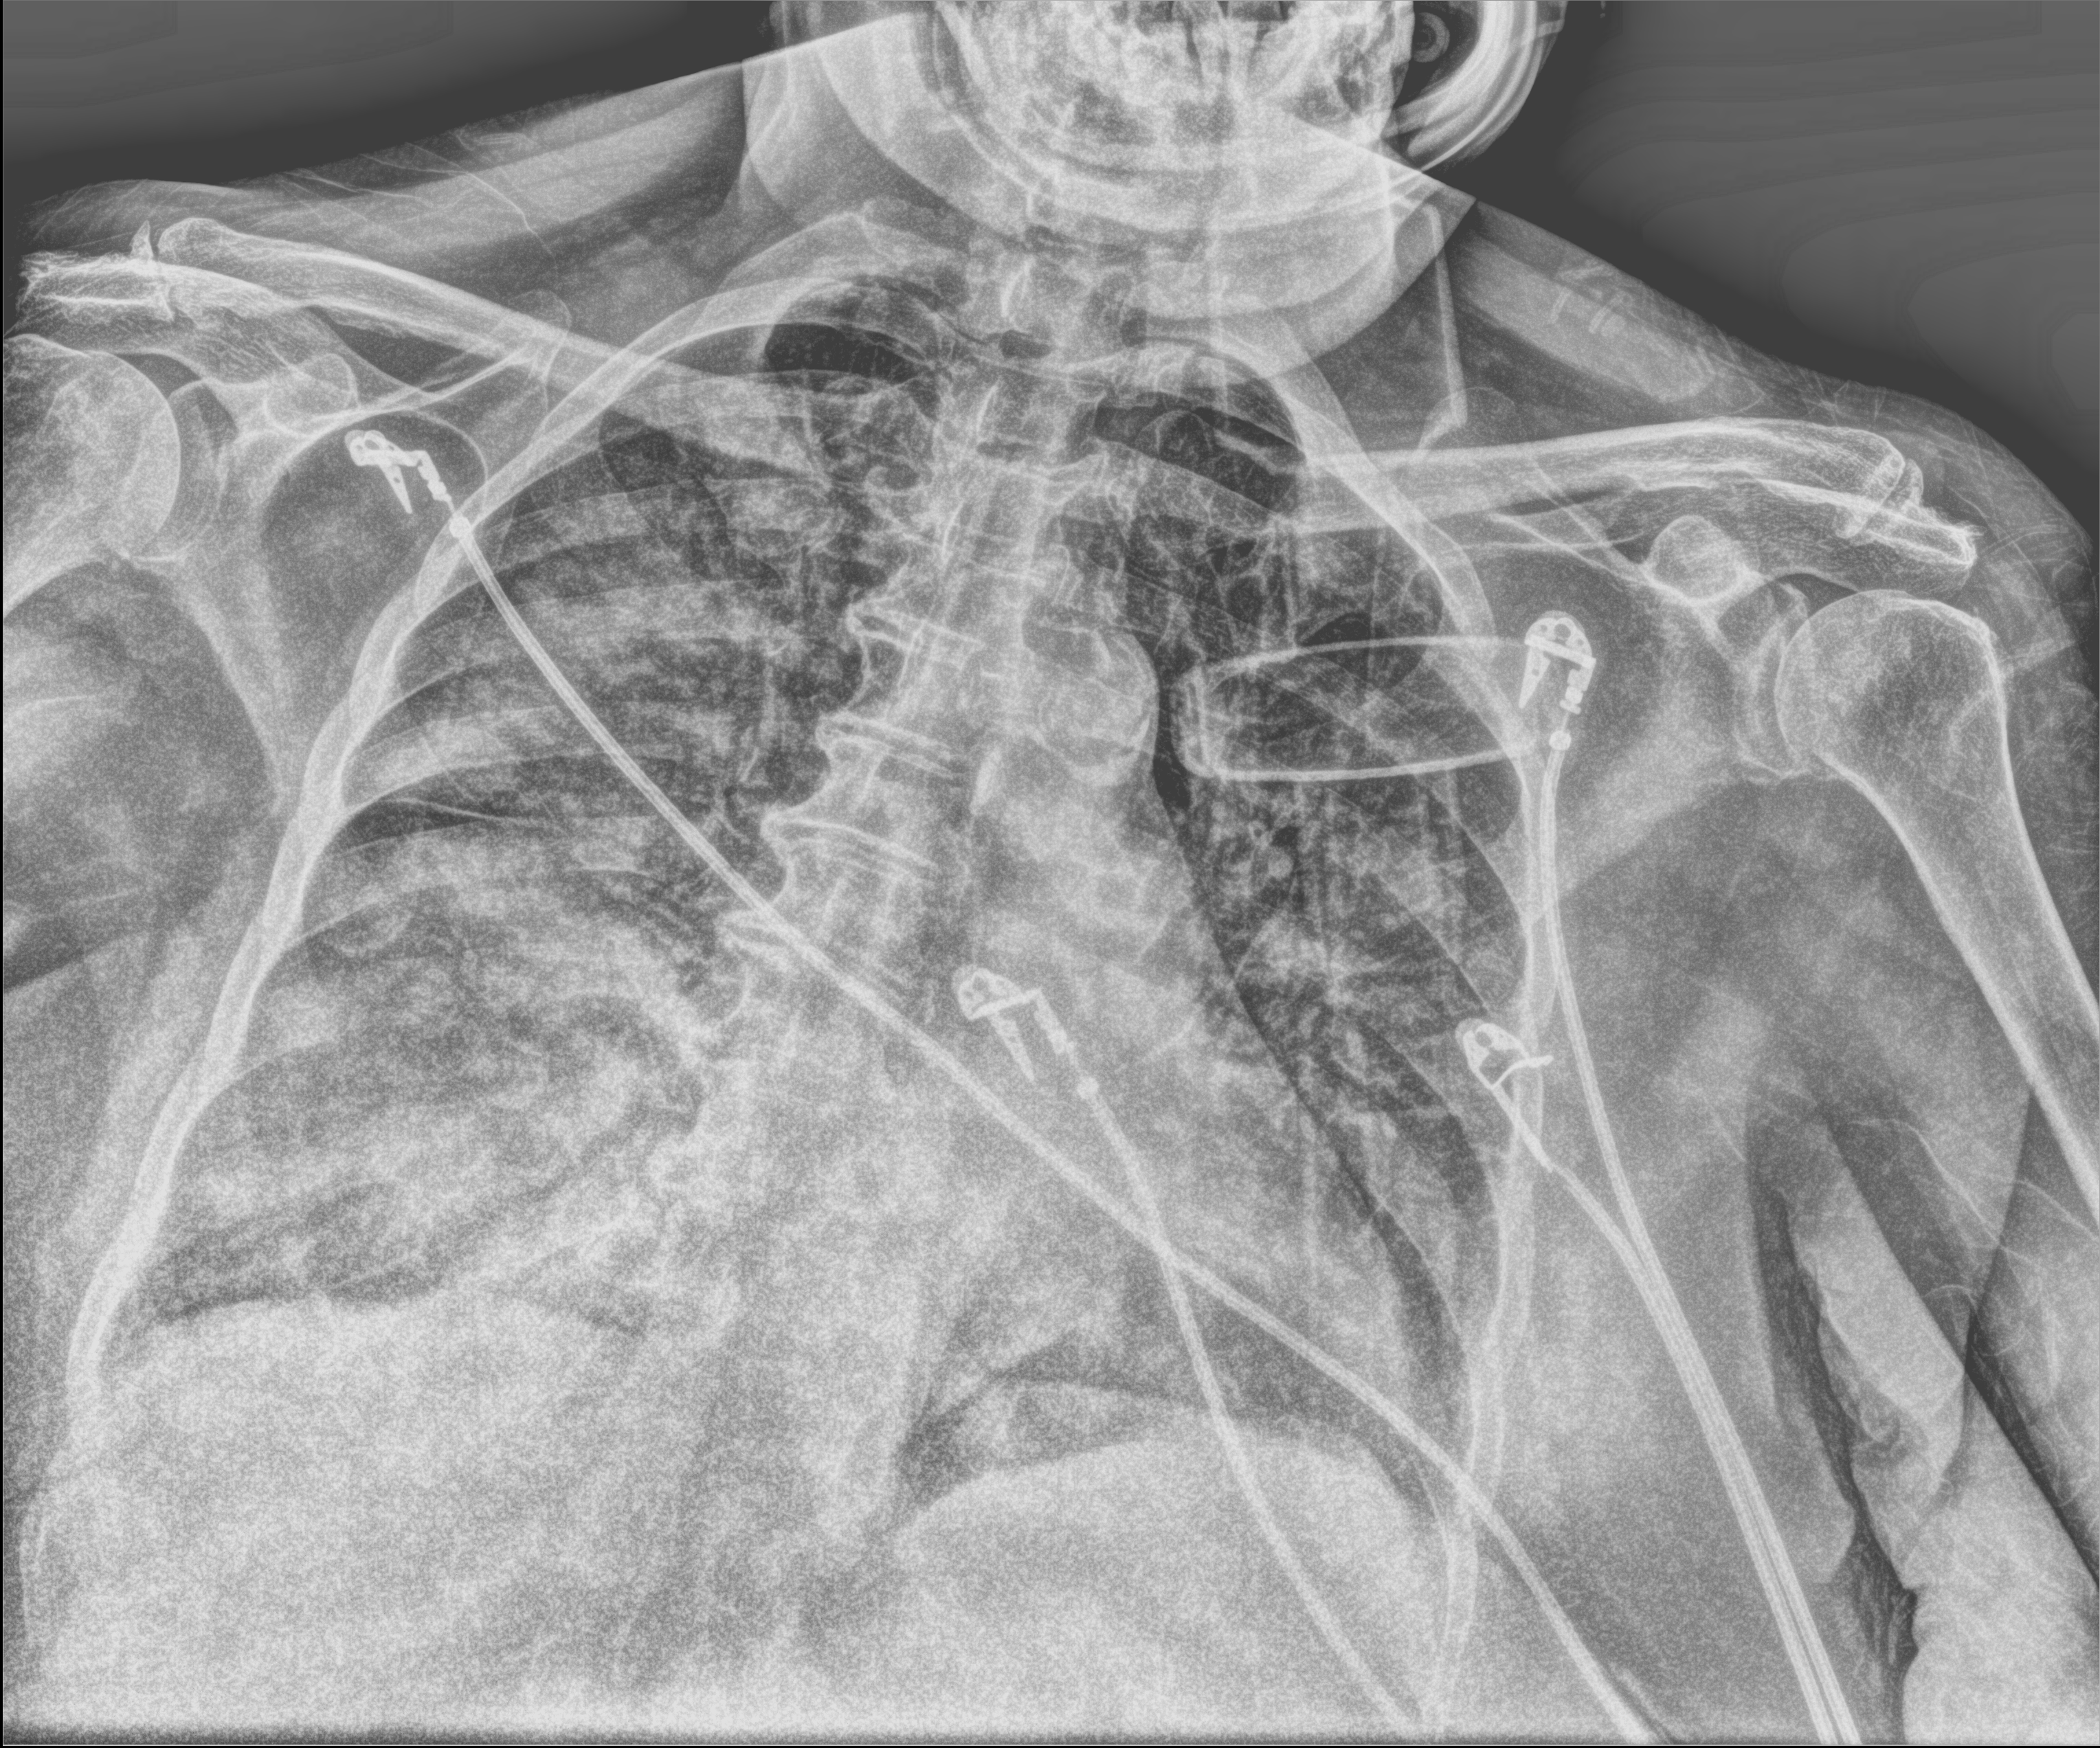
Chest X-ray (portable). Female patient hospitalised with COVID-19, age 75–90 years.
From the hospital-stay record, not from the radiograph (when in the stay this image was taken is not recorded):
- length of hospital stay: 4 days
- admitted to intensive care during this hospital stay: no
- mechanically ventilated during this hospital stay: no